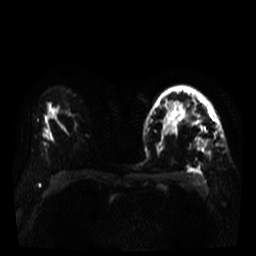
Breast MRI, one axial slice; position 24 of 35 along the scan axis; diffusion-weighted series; image 2 of 4 stored at this slice position (different b-values; order by instance number); 3 T; 5 mm slice thickness; 256 × 256 image matrix. Female patient.
Structures marked on this image (manually delineated by an expert):
- tumour on diffusion-weighted imaging: bounding box [x1, y1, x2, y2] px = [177, 114, 208, 151]